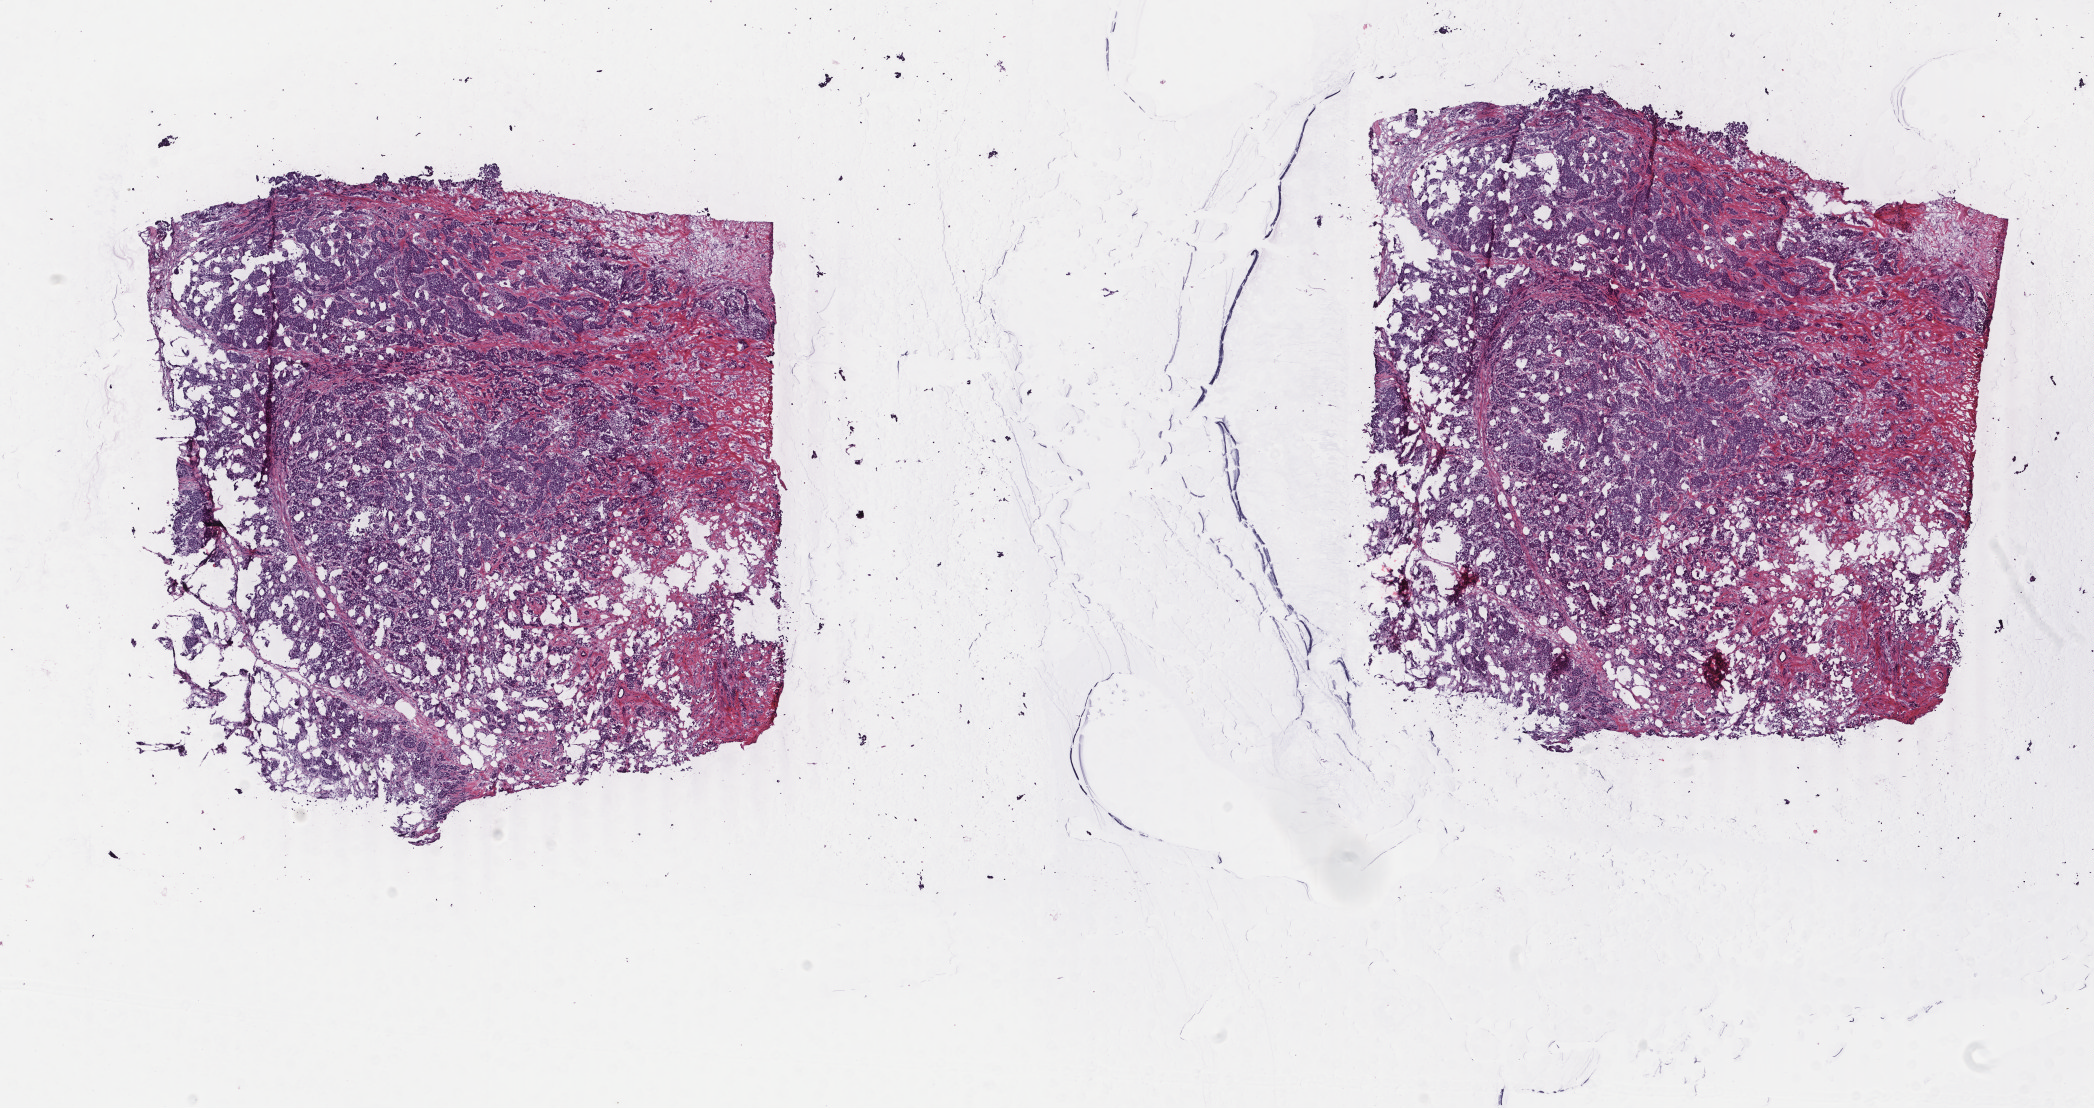
Digitized H&E-stained tissue section (whole slide) — a low-resolution overview of the entire scanned area, about 16.7 x 8.8 mm, frozen section from the top of the tissue portion, primary tumour sample from the breast. Patient: female, age at initial diagnosis 54 years. Composition of this section per pathologist review: tumour cells 100%, tumour nuclei 90%, normal cells 0%, stromal cells 0%, necrosis 0%. Inflammatory infiltration, as recorded: lymphocyte infiltration 0%, monocyte infiltration 0%, neutrophil infiltration 0%.
* AJCC pathologic stage: IIB (6th edition)
* pathologic diagnosis: Infiltrating duct carcinoma, NOS